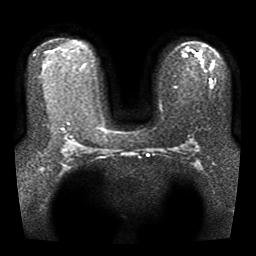
Breast MRI, one axial slice; position 24 of 41 along the scan axis; diffusion-weighted series; image 2 of 4 stored at this slice position (different b-values; order by instance number); 1.5 T; 5 mm slice thickness; 256 × 256 image matrix, field of view 330 × 330 mm. Female patient.
Outlined on this slice (expert manual segmentation):
- tumour on diffusion-weighted imaging: bounding box (x1, y1, x2, y2) in pixels: (196, 54, 200, 58)